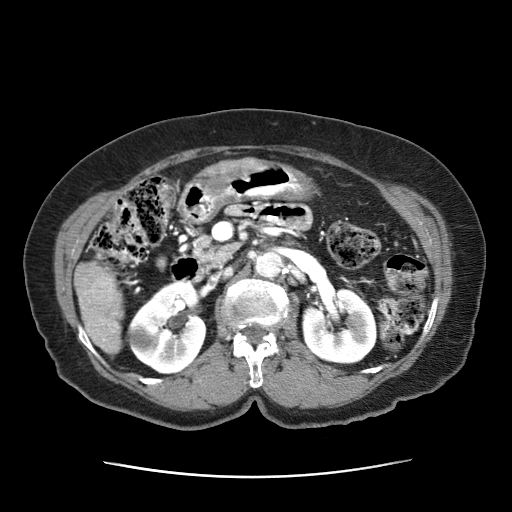
Contrast-enhanced abdominal CT (liver protocol), one axial slice; position 14 of 63 along the scan axis; 120 kVp; intravenous contrast given; soft-tissue window (W 400 / L 40 HU); 2.5 mm slice thickness; 512 × 512 image matrix, field of view 360 × 360 mm. Patient: female, 79 years. From the clinical record (not read from this slice): diagnosis: hepatocellular carcinoma (patient treated with transarterial chemoembolisation; whether this scan precedes or follows treatment is not stated here); TNM stage (as recorded): Stage-II; Child-Pugh class: B; tumour differentiation: well differentiated; tumour size: 5 cm.
Annotated regions visible in this slice (semi-automatic segmentation, software-assisted and operator-edited):
- abdominal aorta: box from (x=254, y=249) to (x=284, y=277) px
- liver parenchyma outside the tumour (the mass and vessels are separate outlines, so this box may not span the whole liver): (x=75, y=261)–(x=125, y=355)
- mass: (x=199, y=162)–(x=239, y=173)
- liver vessels: (x=103, y=338)–(x=105, y=341)